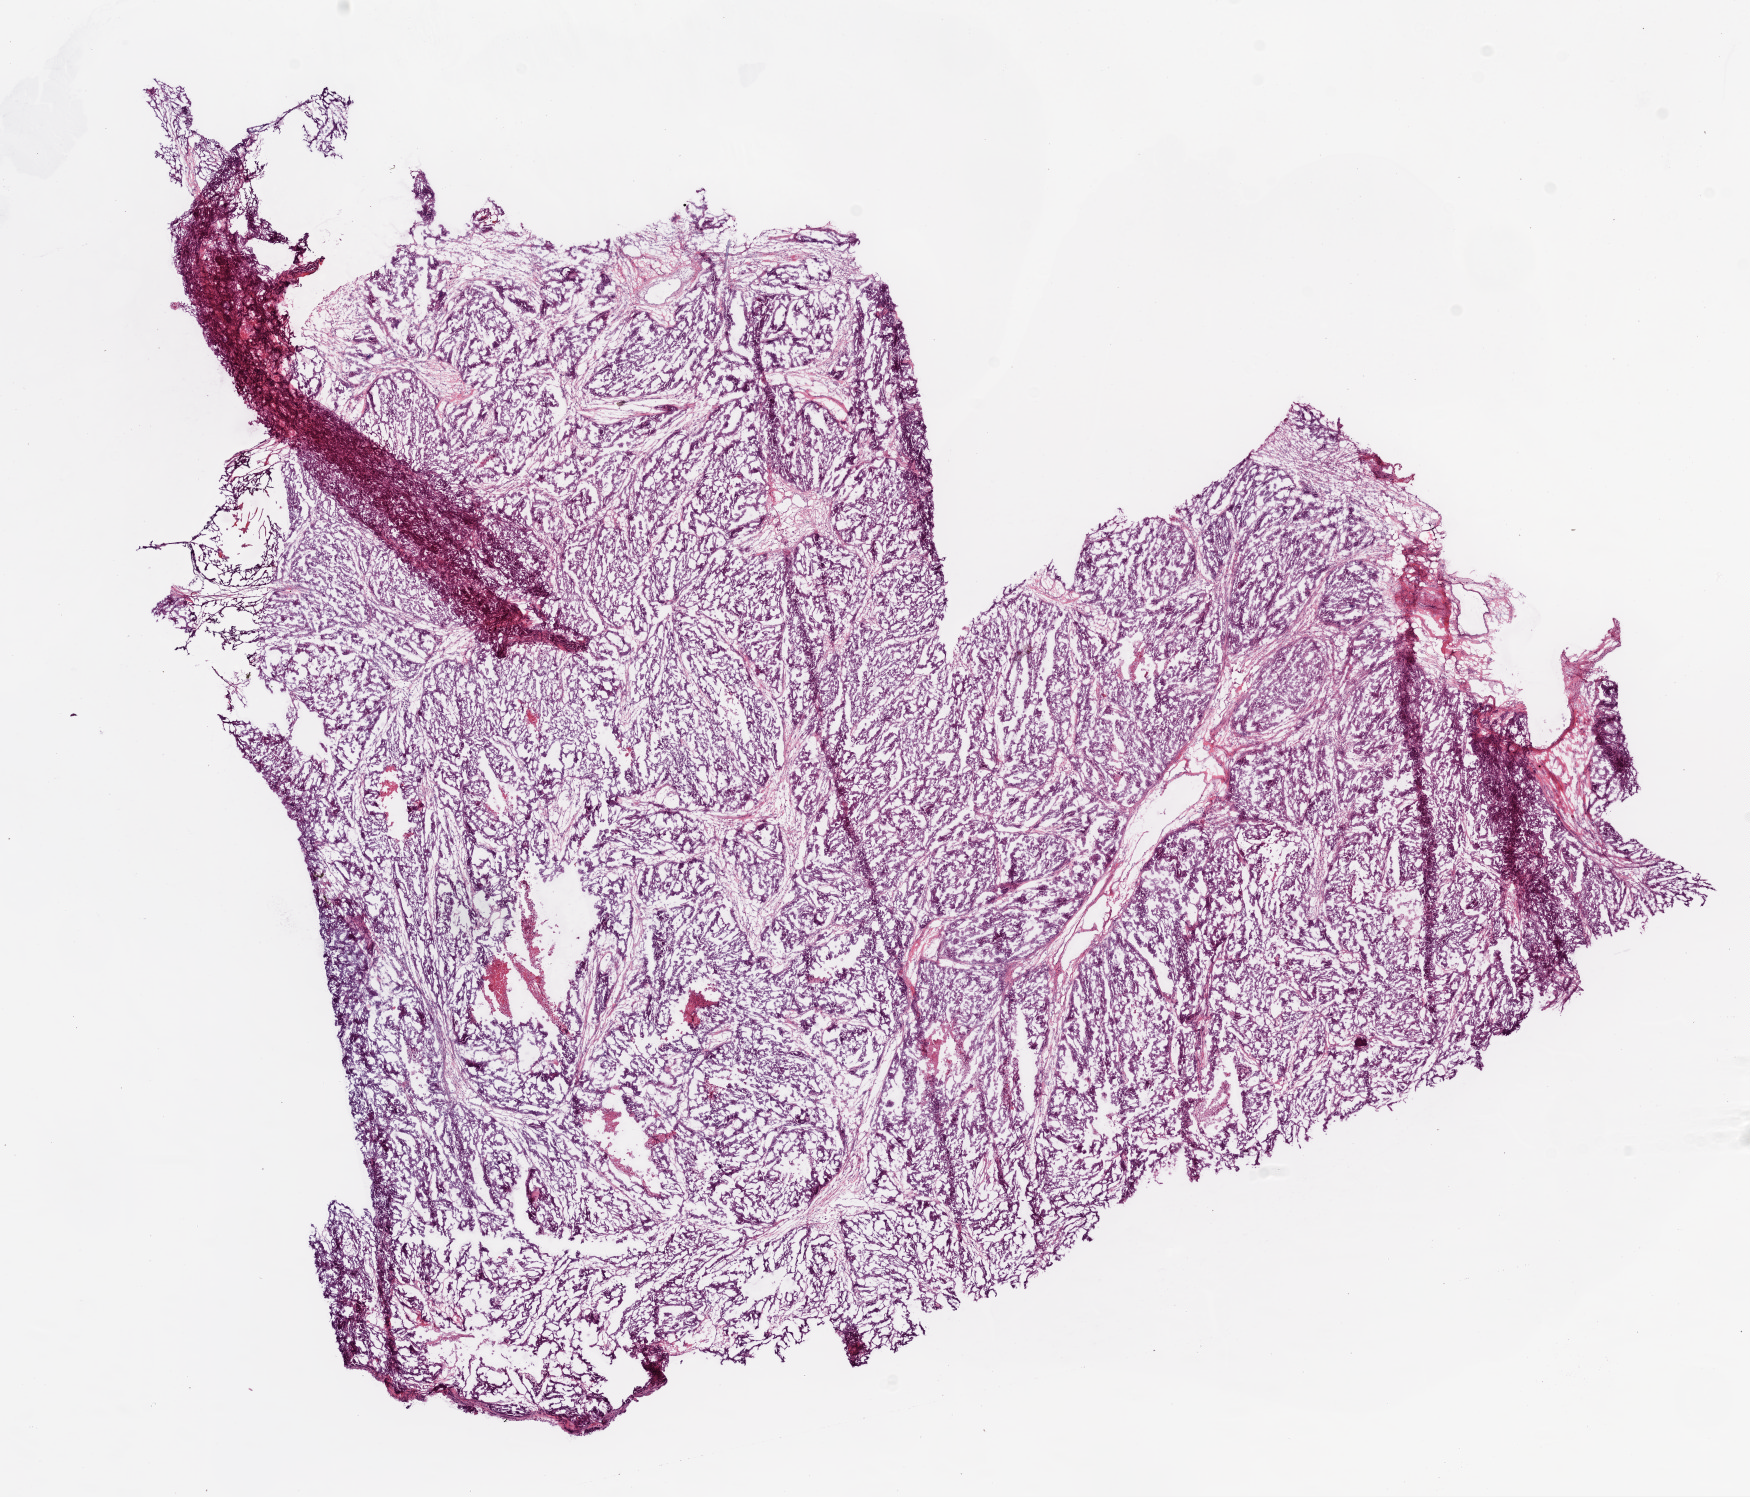
Digitized H&E tissue section (whole slide) — shown as a low-resolution overview of the whole scanned area (about 14.0 x 12.0 mm), frozen section, ovary, primary tumour sample. Female, age 59 years at initial diagnosis. Histologic grade: G3 (poorly differentiated). Composition of this section per pathologist review: tumour cells 85%, tumour nuclei 90%, normal cells 0%, stromal cells 10%, necrosis 5%.
Laterality: bilateral. Diagnosis: Serous cystadenocarcinoma, NOS. FIGO stage: IIIC.